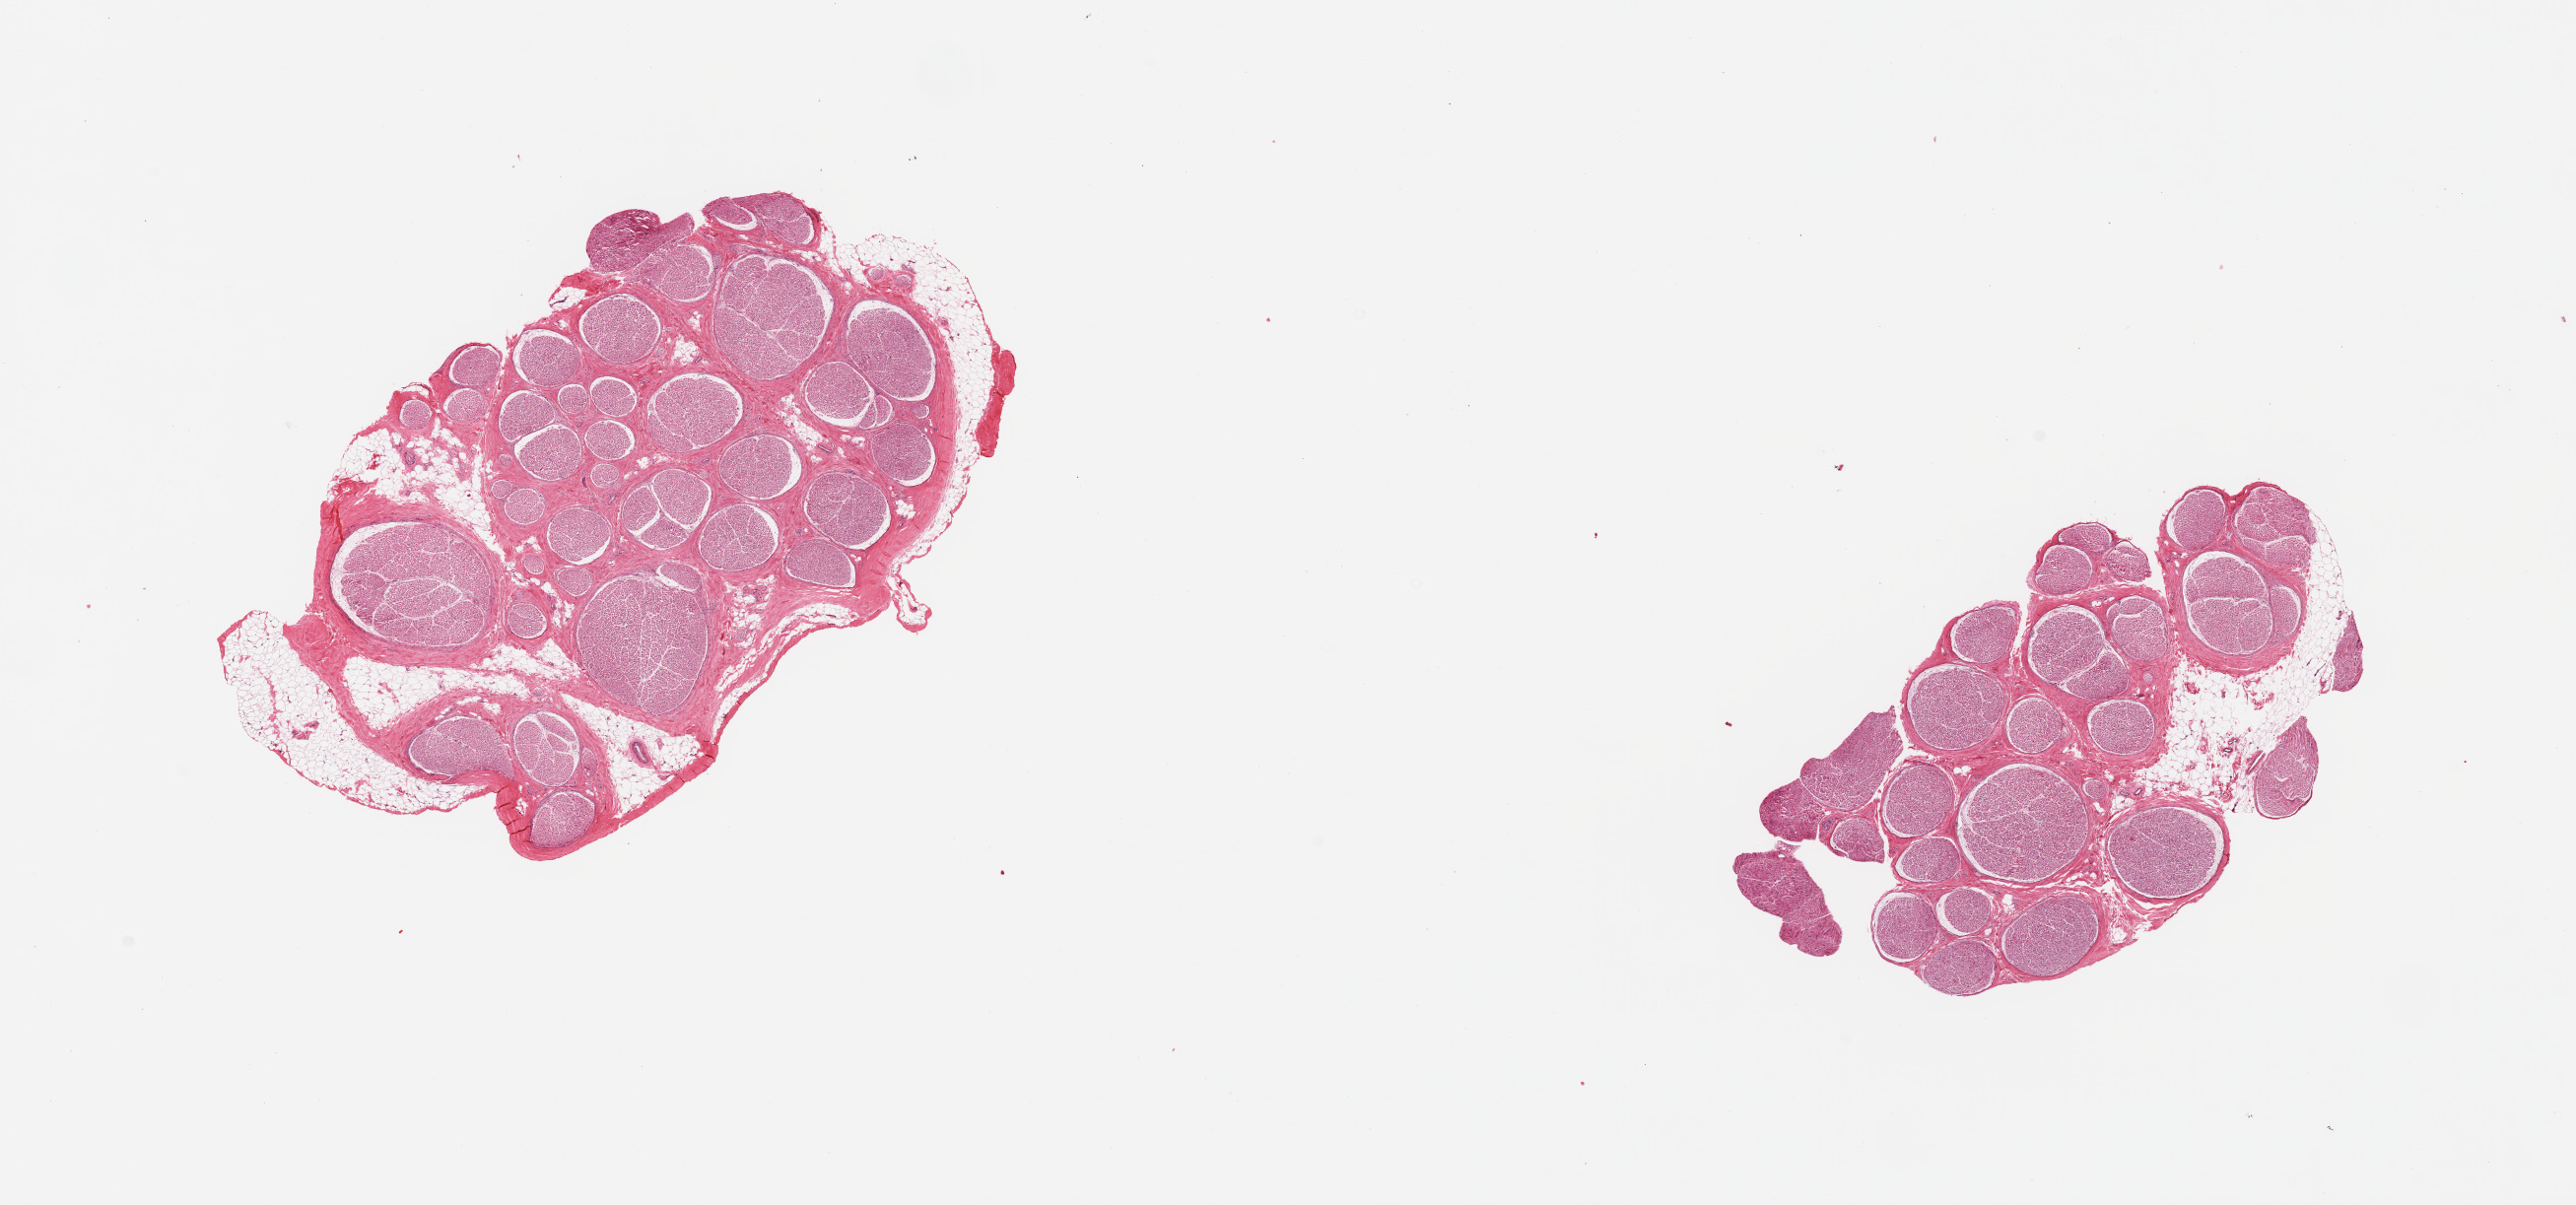
Whole-slide image, haematoxylin and eosin stain, brightfield, shown as a low-resolution overview of the whole scanned area (about 20.7 x 9.7 mm, from a 20x scan); PAXgene-fixed paraffin-embedded (PFPE) section; sampled site (target tissue): tibial nerve; donor tissue sample. Donor: male.
- reviewer comment on this tissue sample: 2 pieces; includes ~15% attached and internal fat